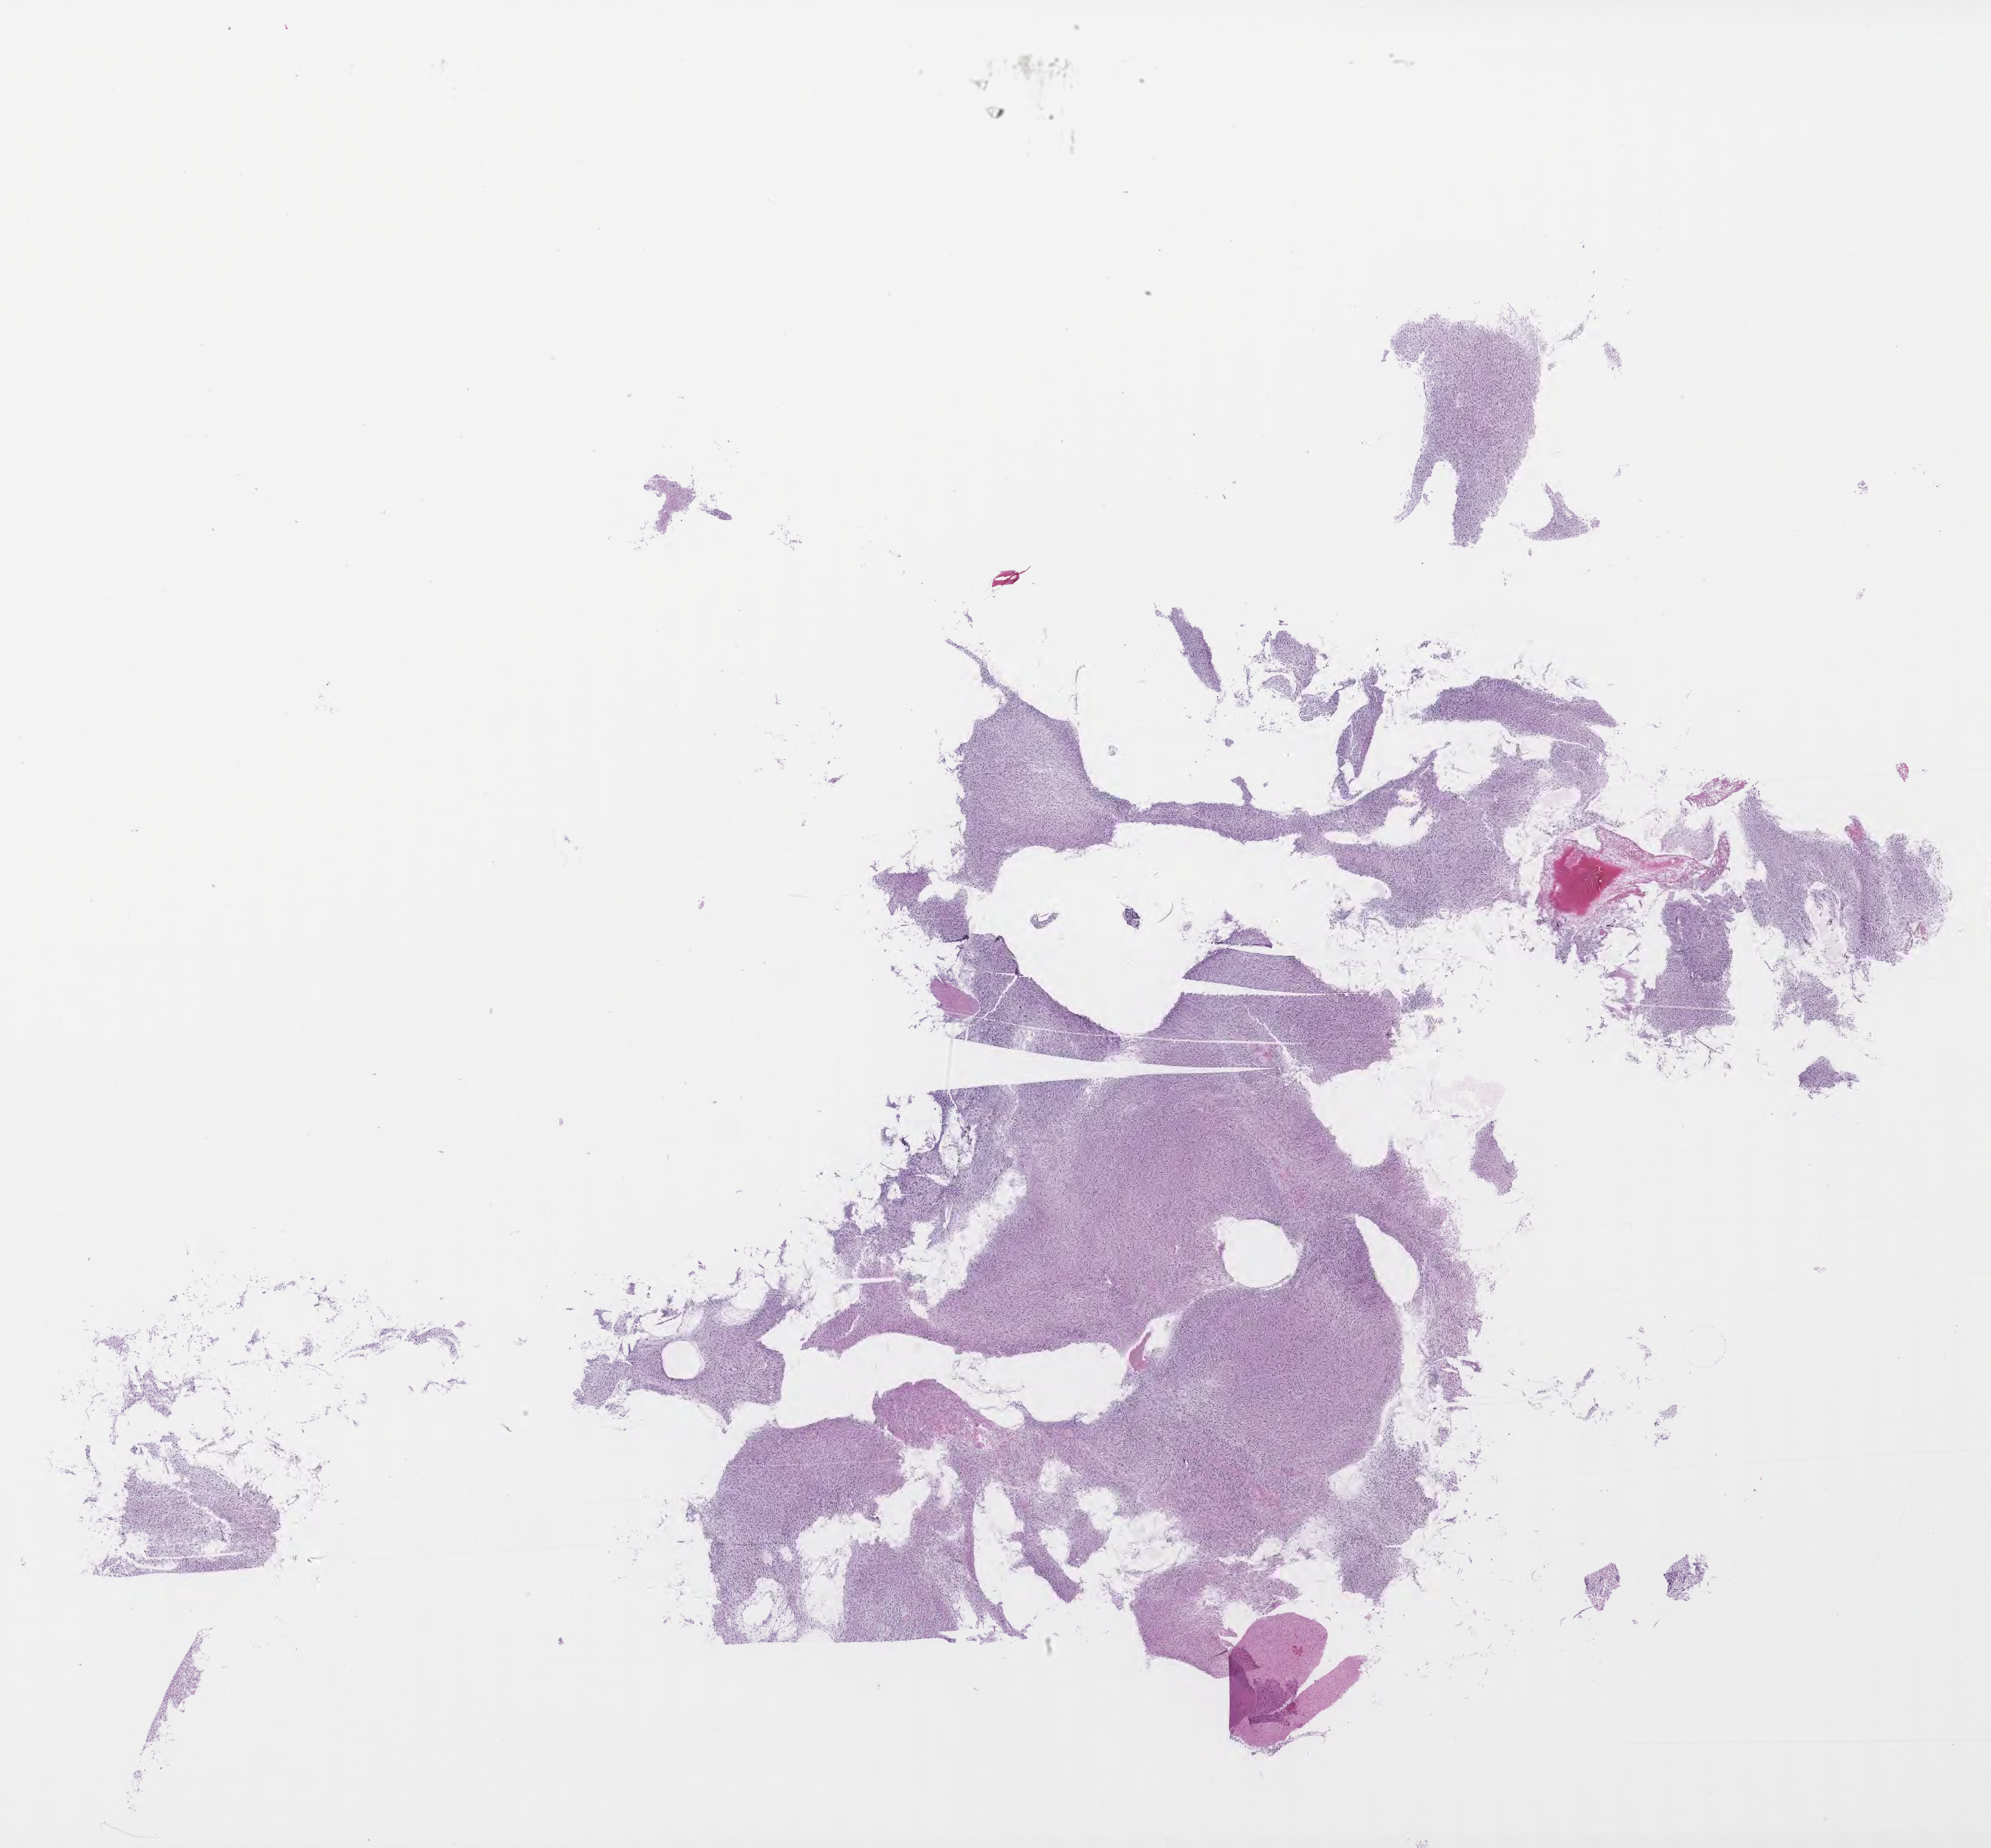
Whole-slide image, H&E stain of tumor tissue from the brain stem, shown as a low-resolution overview of the whole scanned area (about 24.2 x 22.4 mm), formalin-fixed, paraffin-embedded (FFPE) tissue. Patient: male, age 78 months (6 years 6 months).
Recorded diagnosis: Glioma, malignant.